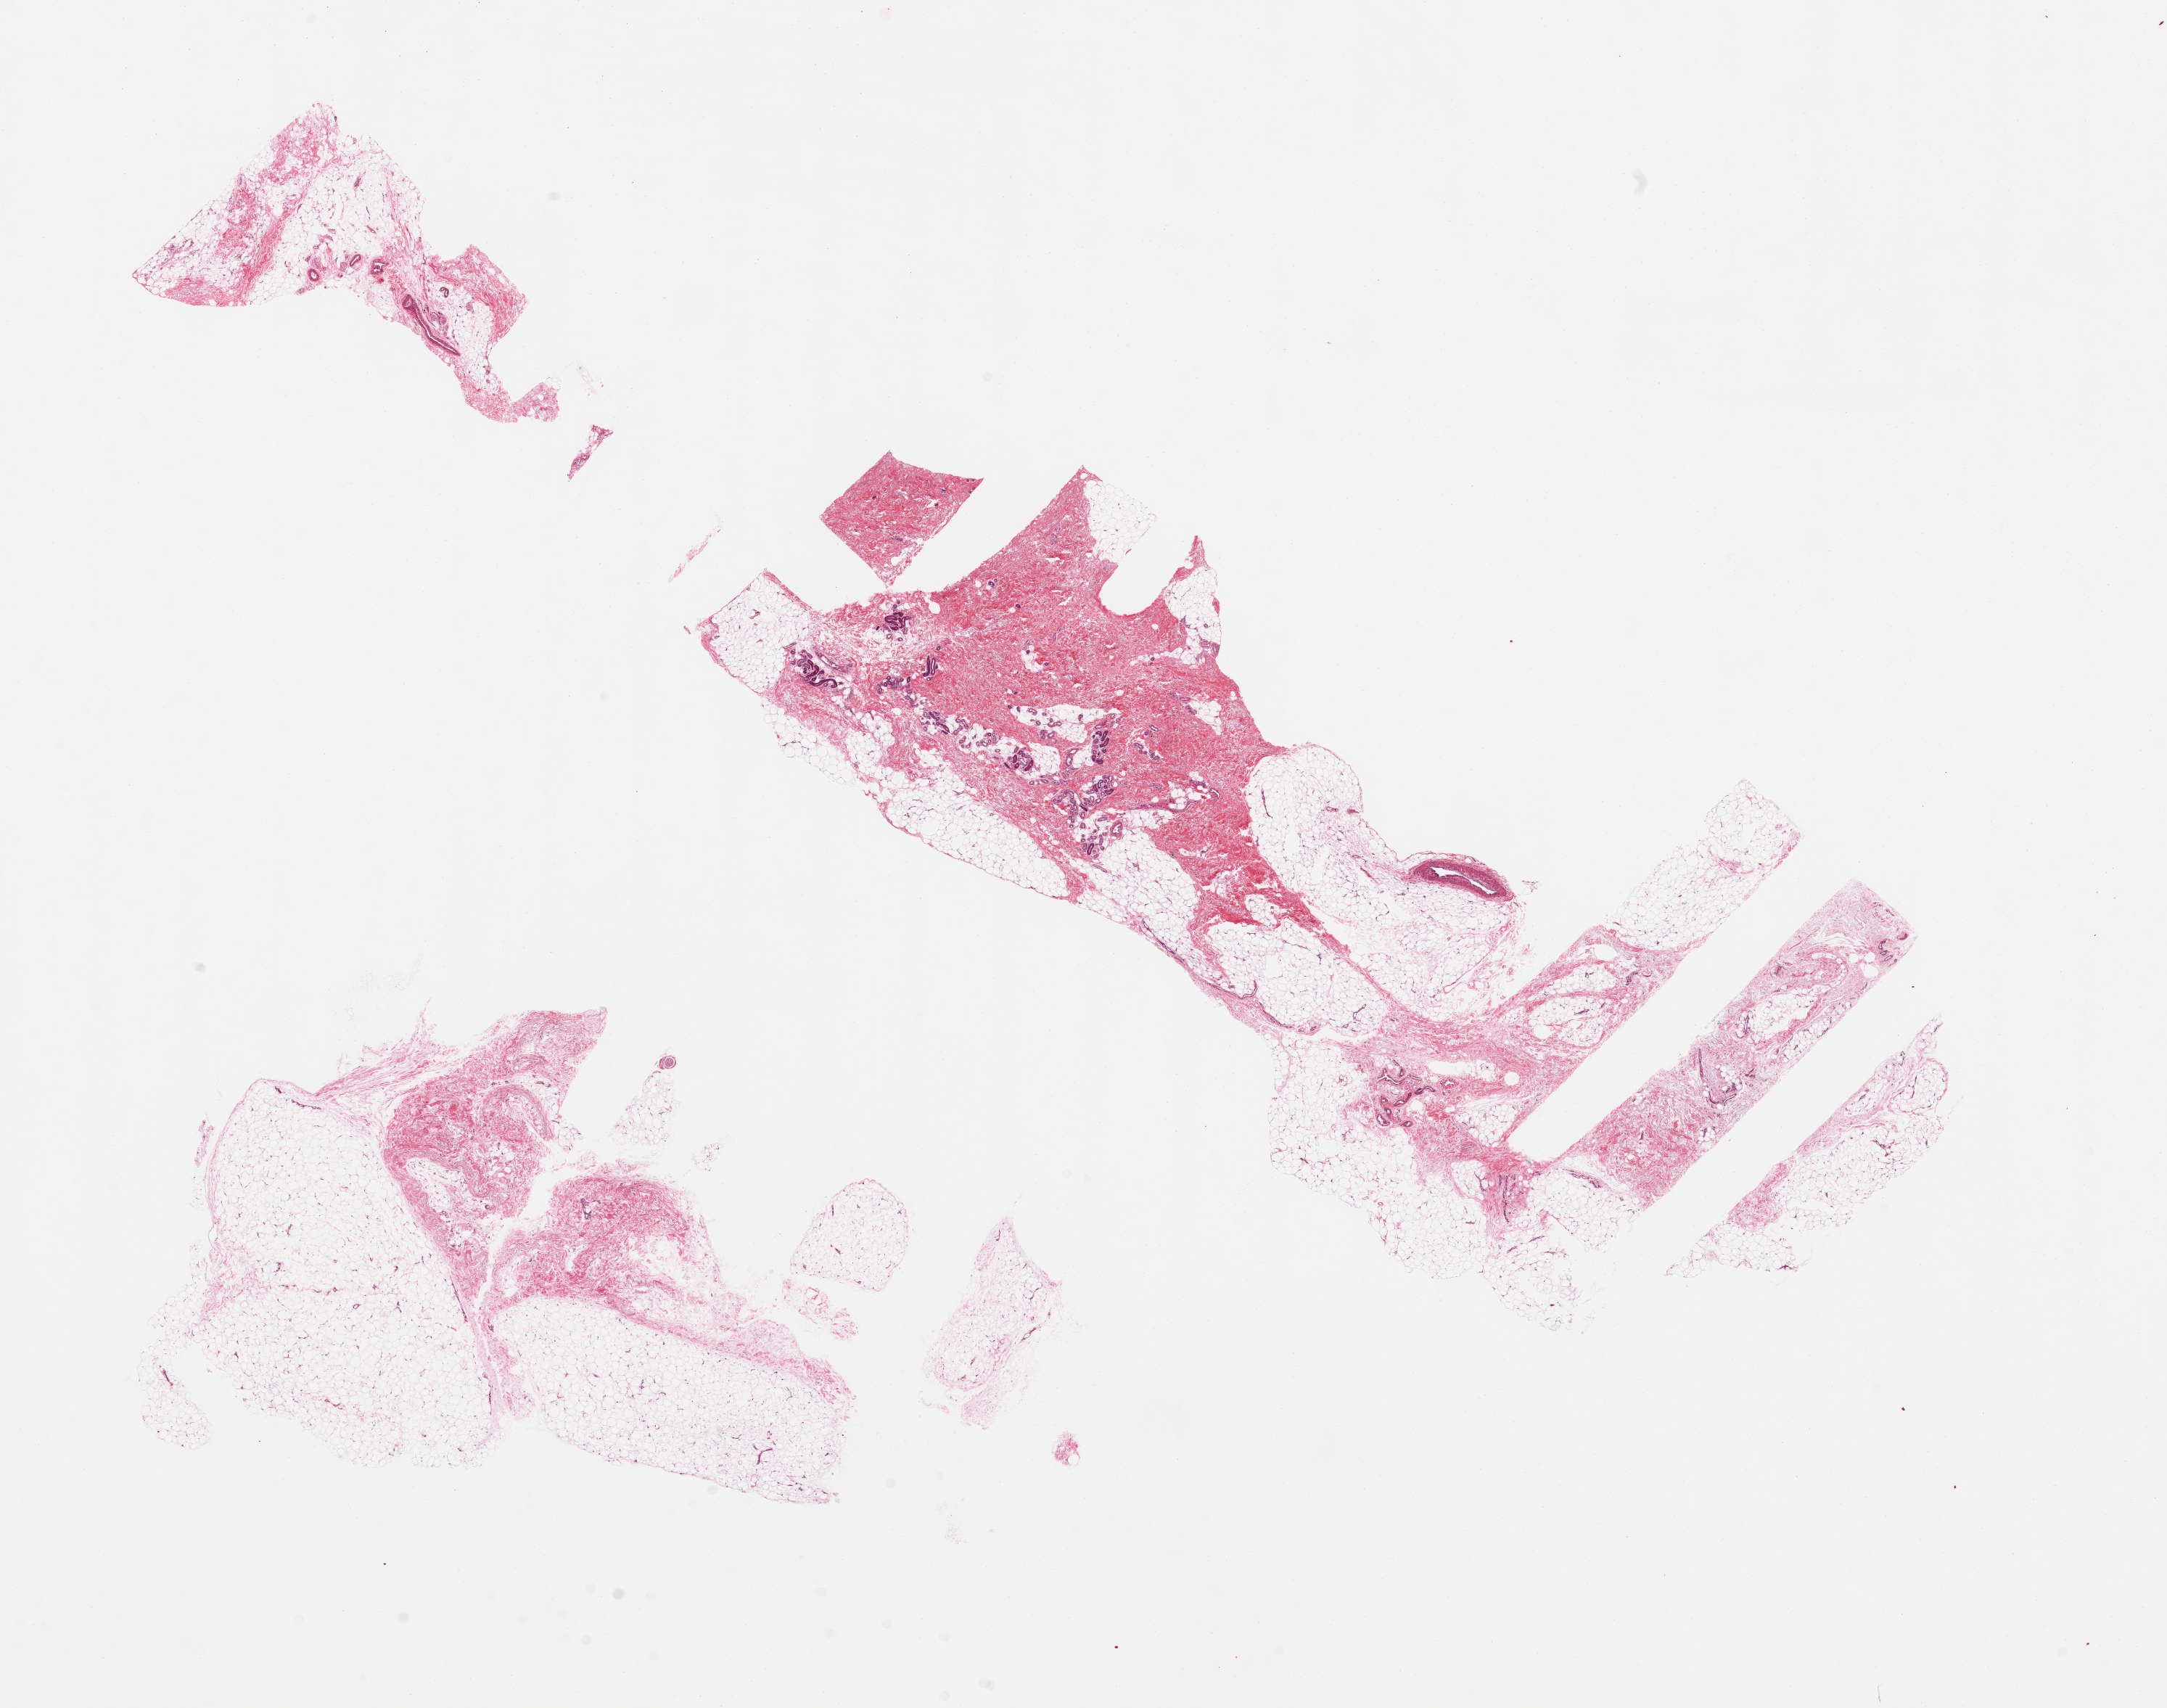
Digitized hematoxylin and eosin (H&E)-stained section, a low-resolution overview of the entire scanned area, about 23.6 x 18.6 mm, PAXgene-fixed, paraffin-embedded tissue, sampled site (target tissue): adipose tissue, tissue donor sample.
• pathologist's review note for this sample: 2 pieces, ~40% intermingled fascia/fibrous tissue